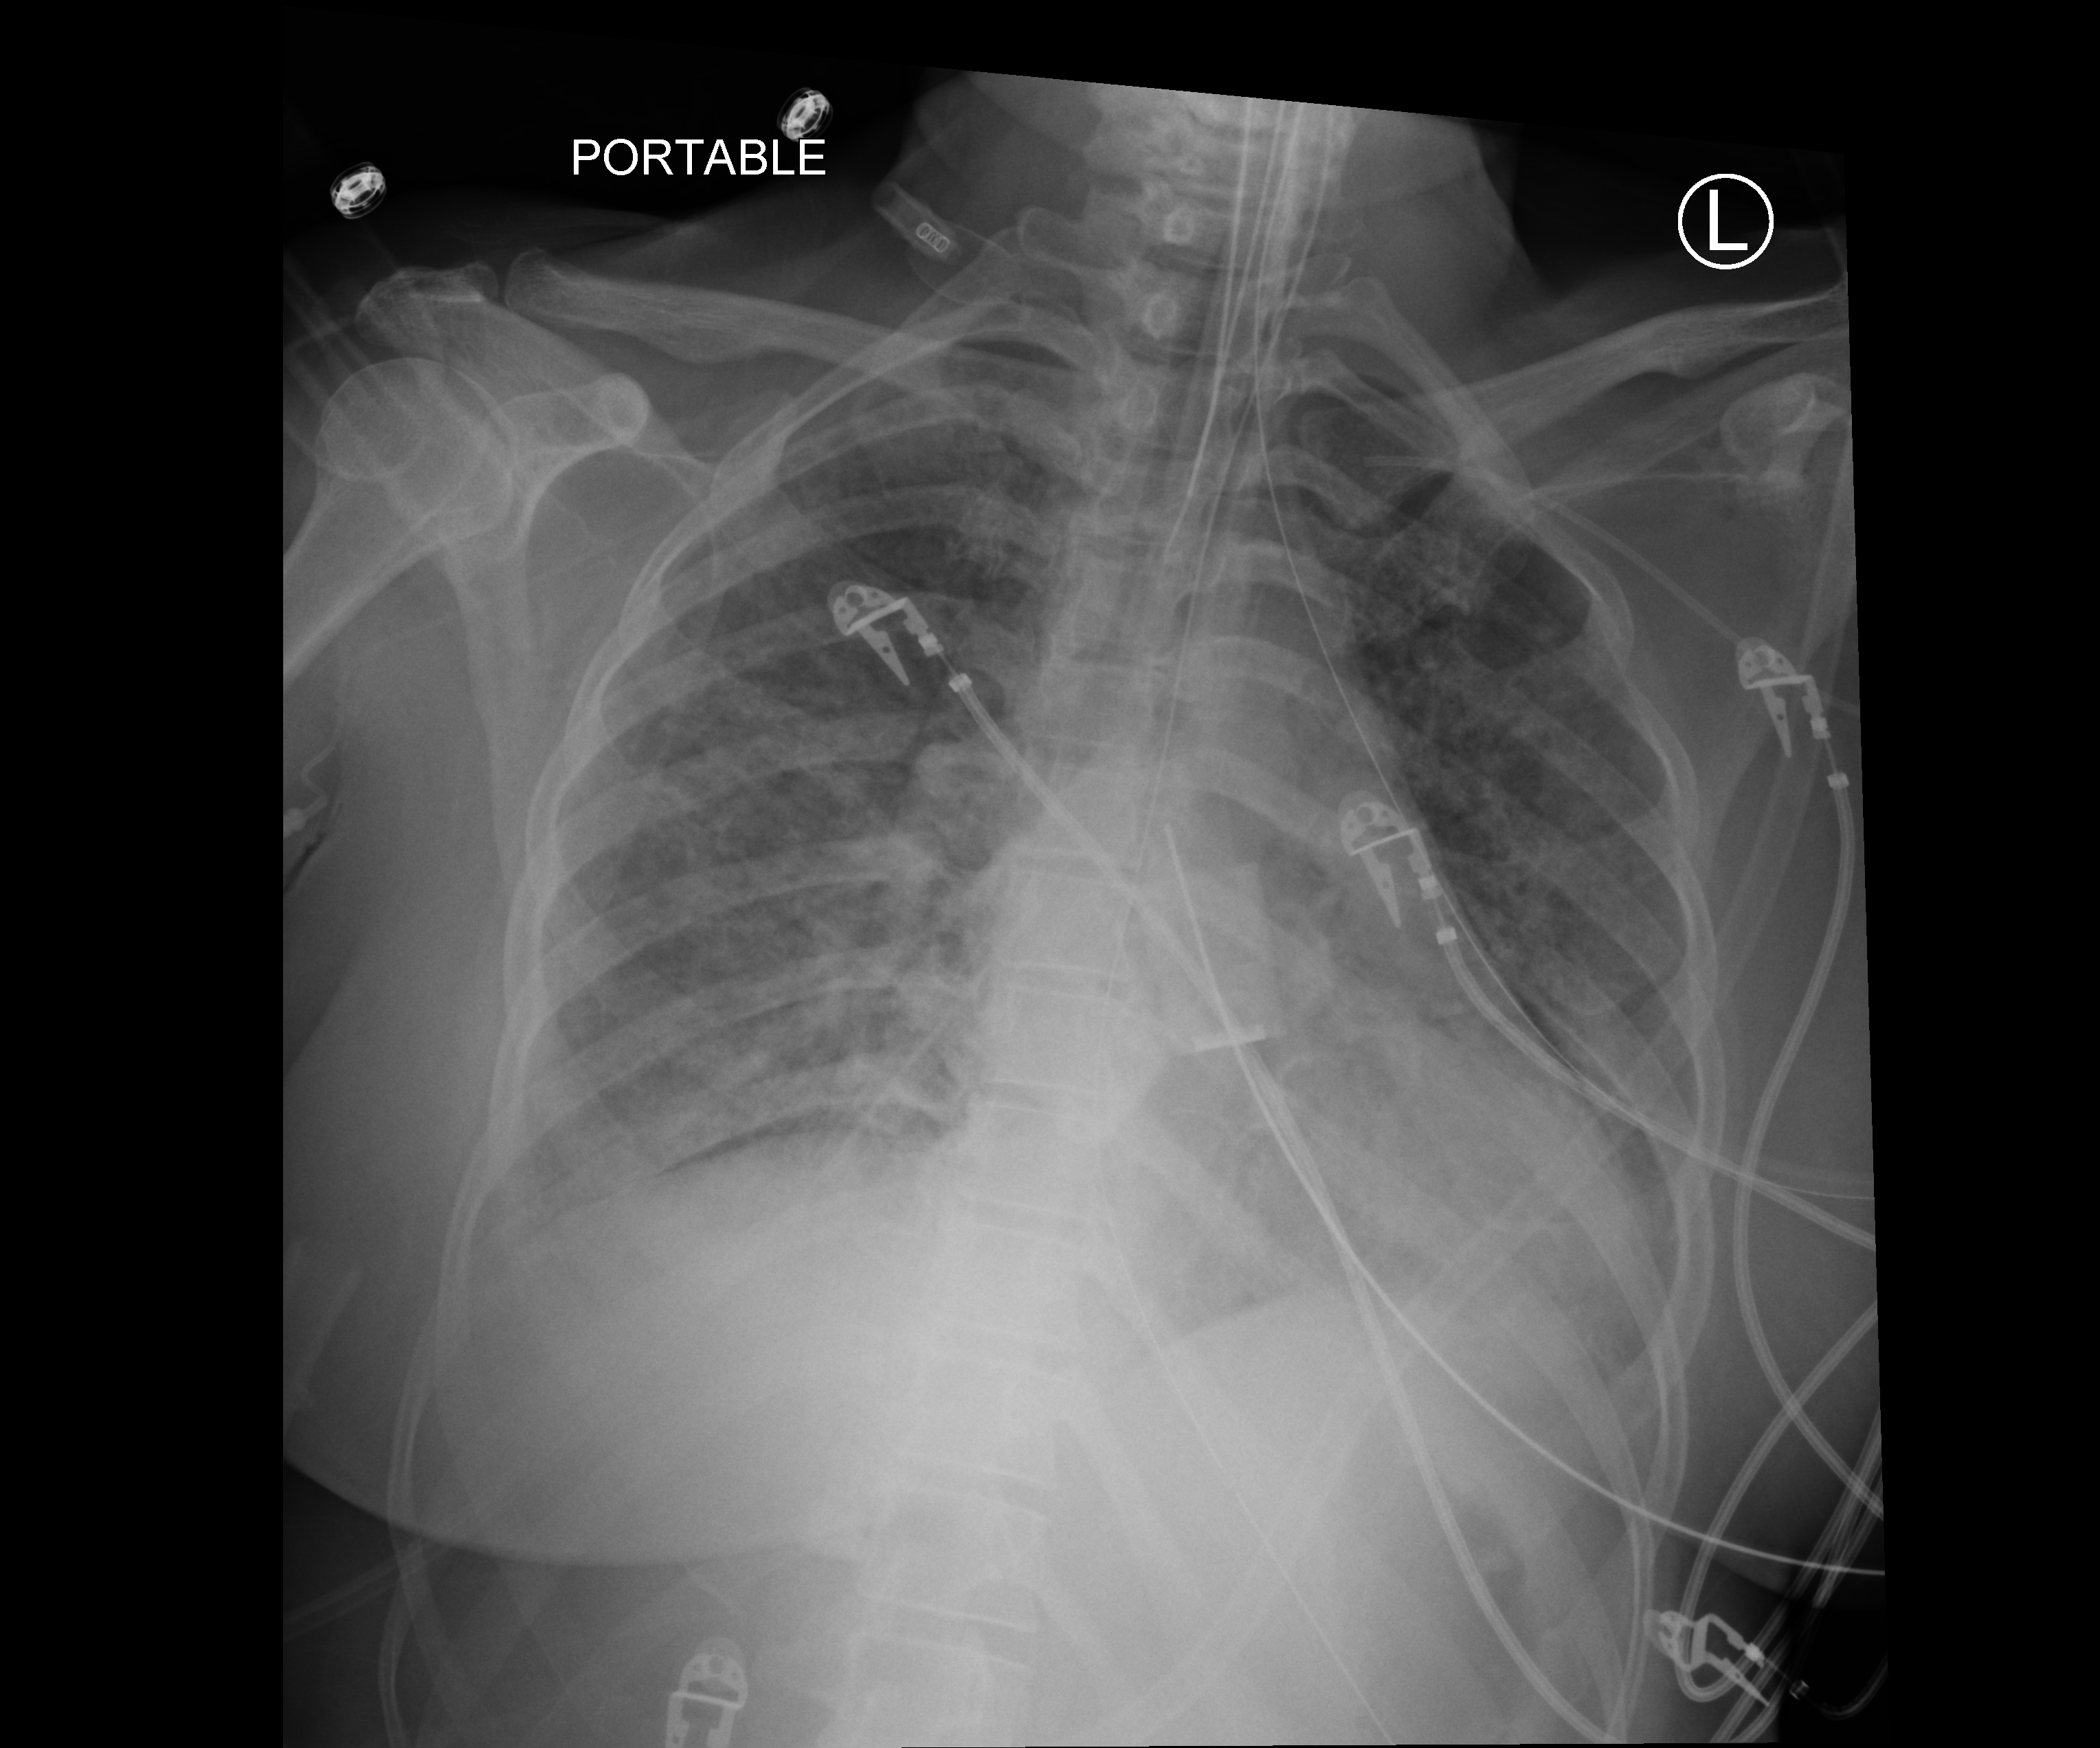
Portable chest radiograph, anteroposterior (AP) projection. Male patient hospitalised with COVID-19, age 18–59 years.
Hospital-stay facts (about this admission, not read from this image; timing relative to this image not recorded): admitted to intensive care during this hospital stay: yes; smoking status (admission record): never.